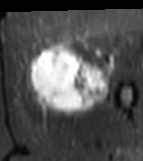
MRI of an extremity soft-tissue mass, one axial slice. Slice 24 of 81 in the series (ordered by position). STIR. MR volume resampled by the dataset authors to the PET/CT grid (not the native acquisition matrix). 3.27 mm slice thickness. 143 × 161 image matrix, field of view 140 × 157 mm. Female patient. Case-level facts recorded for this patient, not image findings: histological type: myxofibrosarcoma; grade: intermediate; site of the primary tumour: left thigh.
Structures marked on this image (expert contour drawn on MRI and transferred to this co-registered scan by the dataset authors):
- gross tumour volume including surrounding oedema: bounding box (x1, y1, x2, y2) in pixels: (26, 40, 114, 116)
- gross tumour volume (mass): (28, 46, 112, 111)